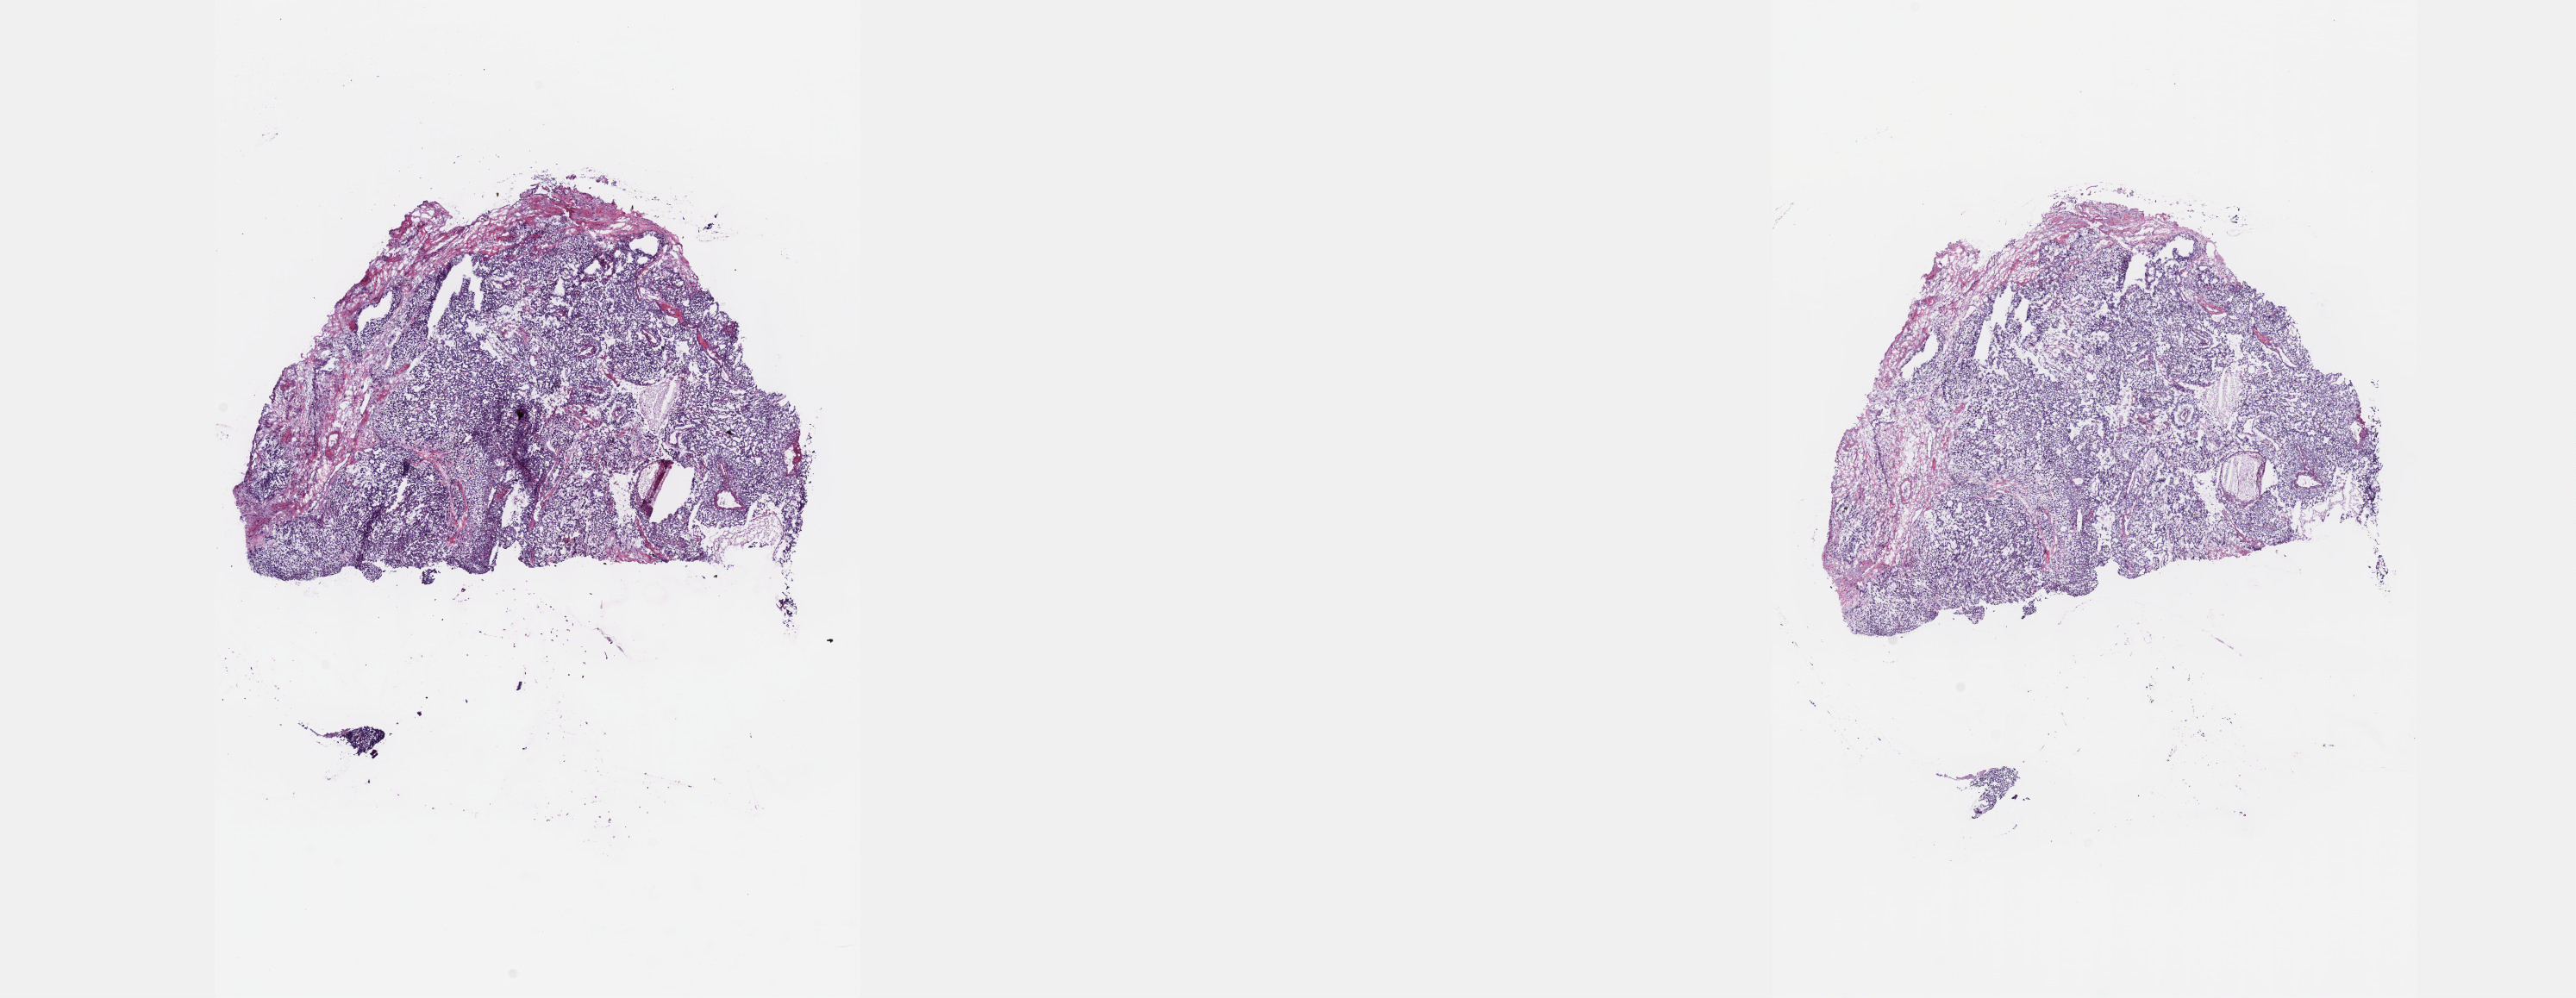
Whole-slide histology image, H&E, shown as a low-resolution overview of the whole scanned area (about 24.1 x 9.4 mm, from a 40x scan), frozen section from the top of the tissue portion, sample: primary tumour, testis. Patient: male, age at initial diagnosis 66 years. Pathologist review of this section (percent, as recorded): tumour cells 75%, tumour nuclei 75%, normal cells 0%, stromal cells 22%, necrosis 3%. Inflammatory infiltration, as recorded: lymphocyte infiltration 3%, monocyte infiltration 2%, neutrophil infiltration 2%.
AJCC pathologic stage: IA (7th edition). Diagnosis: Yolk sac tumor. Laterality: left.